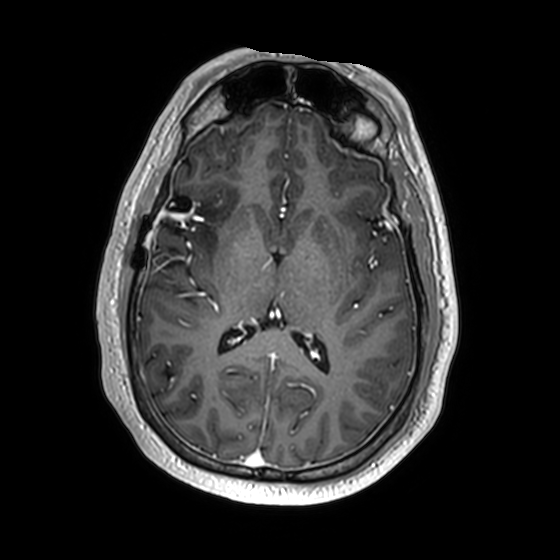
Brain MRI from a brain-tumour surgery series, one axial slice. Position 86 of 174 along the scan axis. T1-weighted post-contrast. 560 × 560 image matrix, field of view 256 × 256 mm. From the clinical record (not read from this slice): histopathology: Astrocytoma; WHO grade: 2; IDH mutation: yes; tumour location: Right Insular.
Structures marked on this image (expert manual segmentation):
- previous resection cavity: box from (x=165, y=195) to (x=192, y=221) px